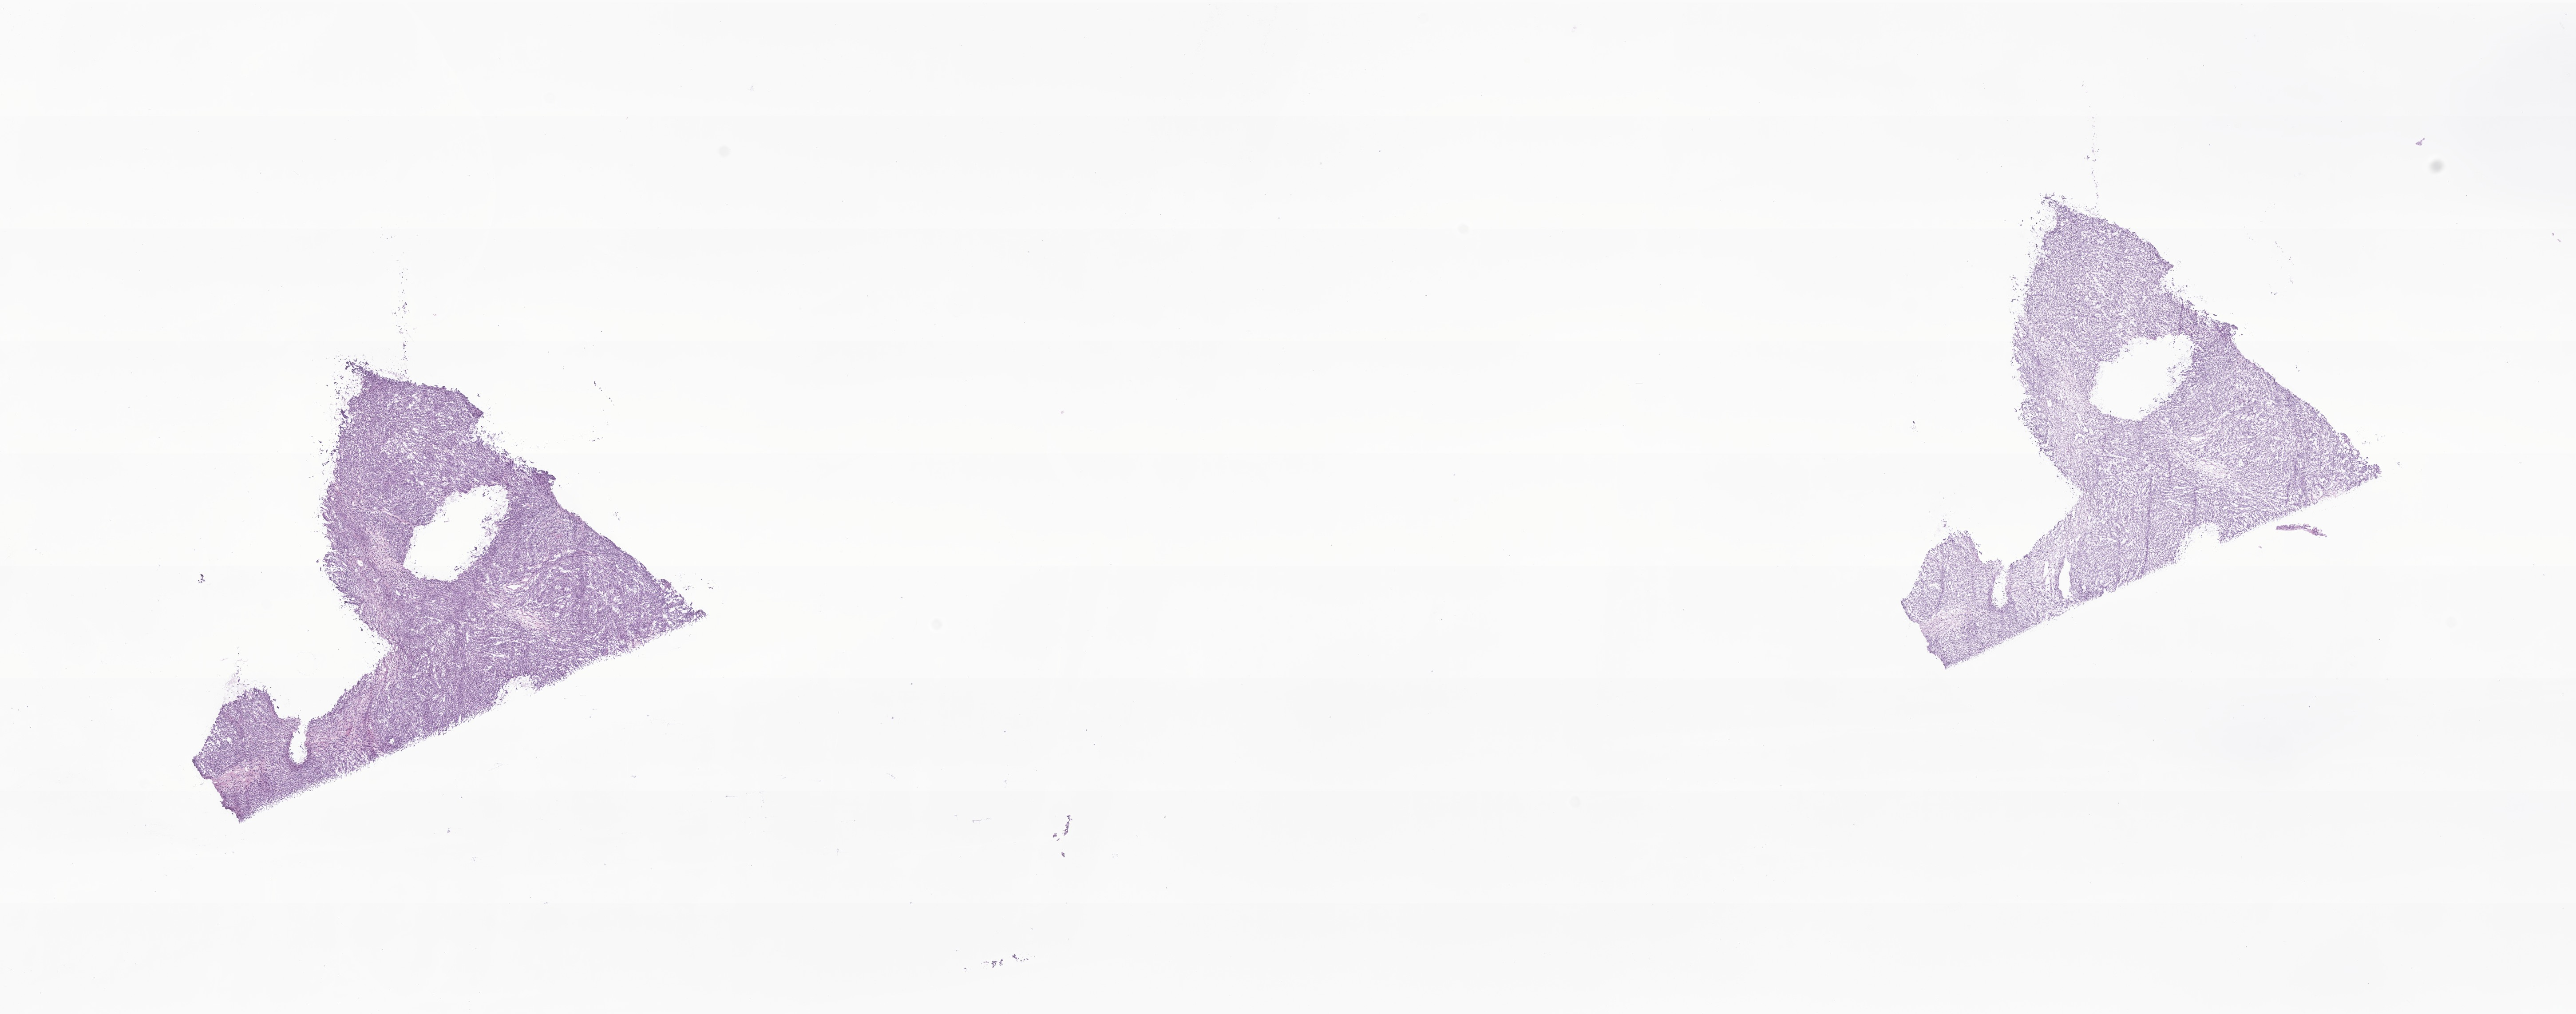
Digitized haematoxylin and eosin-stained section of tumor tissue from the soft tissue of pelvis, whole scanned area (about 24.5 x 9.6 mm) shown as a low-resolution overview, frozen section. Patient female; age 985 days (about 2.7 years).
* recorded diagnosis: Embryonal rhabdomyosarcoma, NOS
* tissue or organ of origin (case record): connective, subcutaneous and other soft tissues of pelvis